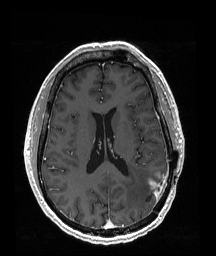
Brain MRI from a brain-tumour surgery series, one axial slice; slice 80 of 192 in the series (ordered by position); T1-weighted post-contrast; 1 mm slice thickness; 216 × 256 image matrix. From the clinical record (not read from this slice): histopathology: Glioblastoma; WHO grade: 4; IDH mutation: no; tumour location: Left Temporoparietal.
Annotated regions visible in this slice (expert manual segmentation):
- tumour: box from (x=150, y=177) to (x=164, y=197) px